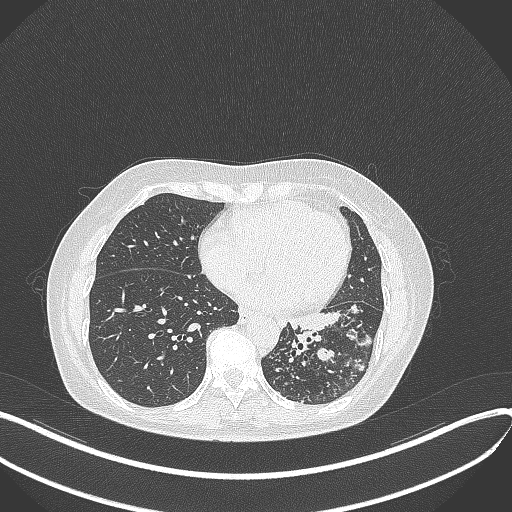
Chest CT, one axial slice. Position 151 of 429 along the scan axis. Reconstruction kernel B70f. Lung window (W 1500 / L -600 HU). 1 mm slice thickness. 512 × 512 image matrix. Female patient, age 63 years. From the clinical record (not read from this slice): clinical TNM (as recorded): T1b N0 M0; histopathological grade: G2-3.
Structures marked on this image (bounding box drawn by a radiologist):
- lung tumour (recorded histology: adenocarcinoma): bounding box <276,302,345,342> (left, top, right, bottom; pixels)